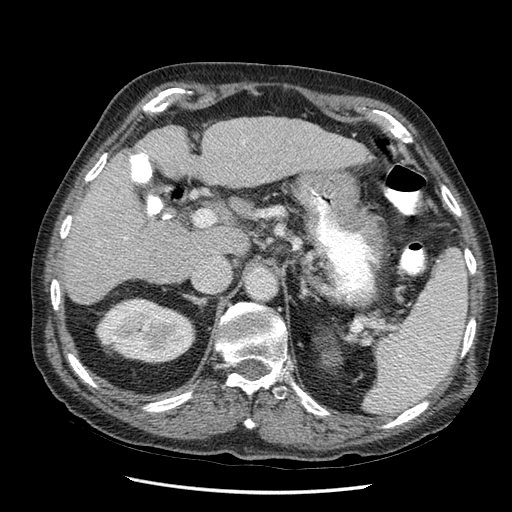
Contrast-enhanced abdominal CT (liver protocol), one axial slice. Reconstruction kernel STANDARD. 120 kVp. Soft-tissue window (W 400 / L 40 HU). 2.5 mm slice thickness. 512 × 512 image matrix, field of view 360 × 360 mm. From the clinical record (not read from this slice): diagnosis: hepatocellular carcinoma (patient treated with transarterial chemoembolisation; whether this scan precedes or follows treatment is not stated here); TNM stage (as recorded): Stage-I; Child-Pugh class: A; tumour differentiation: moderately differentiated.
Annotated regions visible in this slice (semi-automatic segmentation, software-assisted and operator-edited):
- liver parenchyma outside the tumour (the mass and vessels are separate outlines, so this box may not span the whole liver): bounding box [x1, y1, x2, y2] px = [64, 118, 362, 306]
- liver vessels: [121, 243, 126, 245]